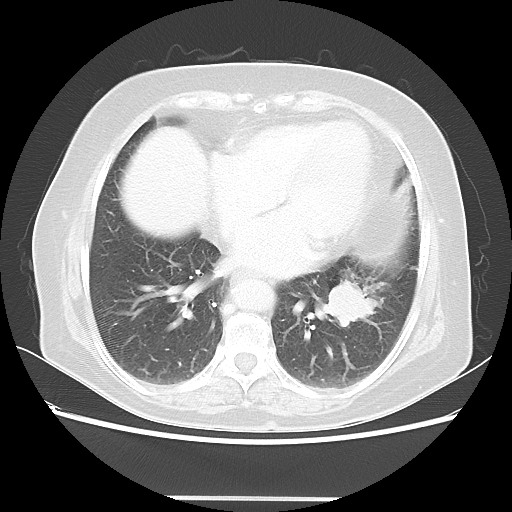
Chest CT, one axial slice. Slice 22 of 56 in the series (ordered by position). Reconstruction kernel LUNG. Lung window (W 1500 / L -600 HU). 512 × 512 image matrix, field of view 360 × 360 mm. Female patient, age 73 years. From the clinical record (not read from this slice): clinical TNM (as recorded): T1c N0 M0.
Outlined on this slice (bounding box drawn by a radiologist):
- lung tumour (recorded histology: adenocarcinoma): box from (x=322, y=278) to (x=389, y=333) px